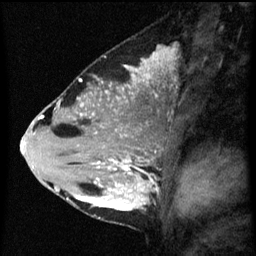
Breast MRI (dynamic contrast-enhanced), one sagittal slice. Dynamic contrast-enhanced series, image 2 of 3 at this slice position (ordered by acquisition). 1.5 T. TE 4.2 ms, TR 8 ms. 256 × 256 image matrix. Female patient, age 33 years.
Outlined on this slice (semi-automatic segmentation, software-assisted and operator-edited):
- analysis volume of interest (the breast-tissue region the enhancement analysis was run in; not a lesion): bounding box (x1, y1, x2, y2) in pixels: (71, 118, 162, 217)
- tumour enhancement mask (voxels above the 70 % enhancement threshold inside the analysis volume of interest): (76, 130, 153, 211)